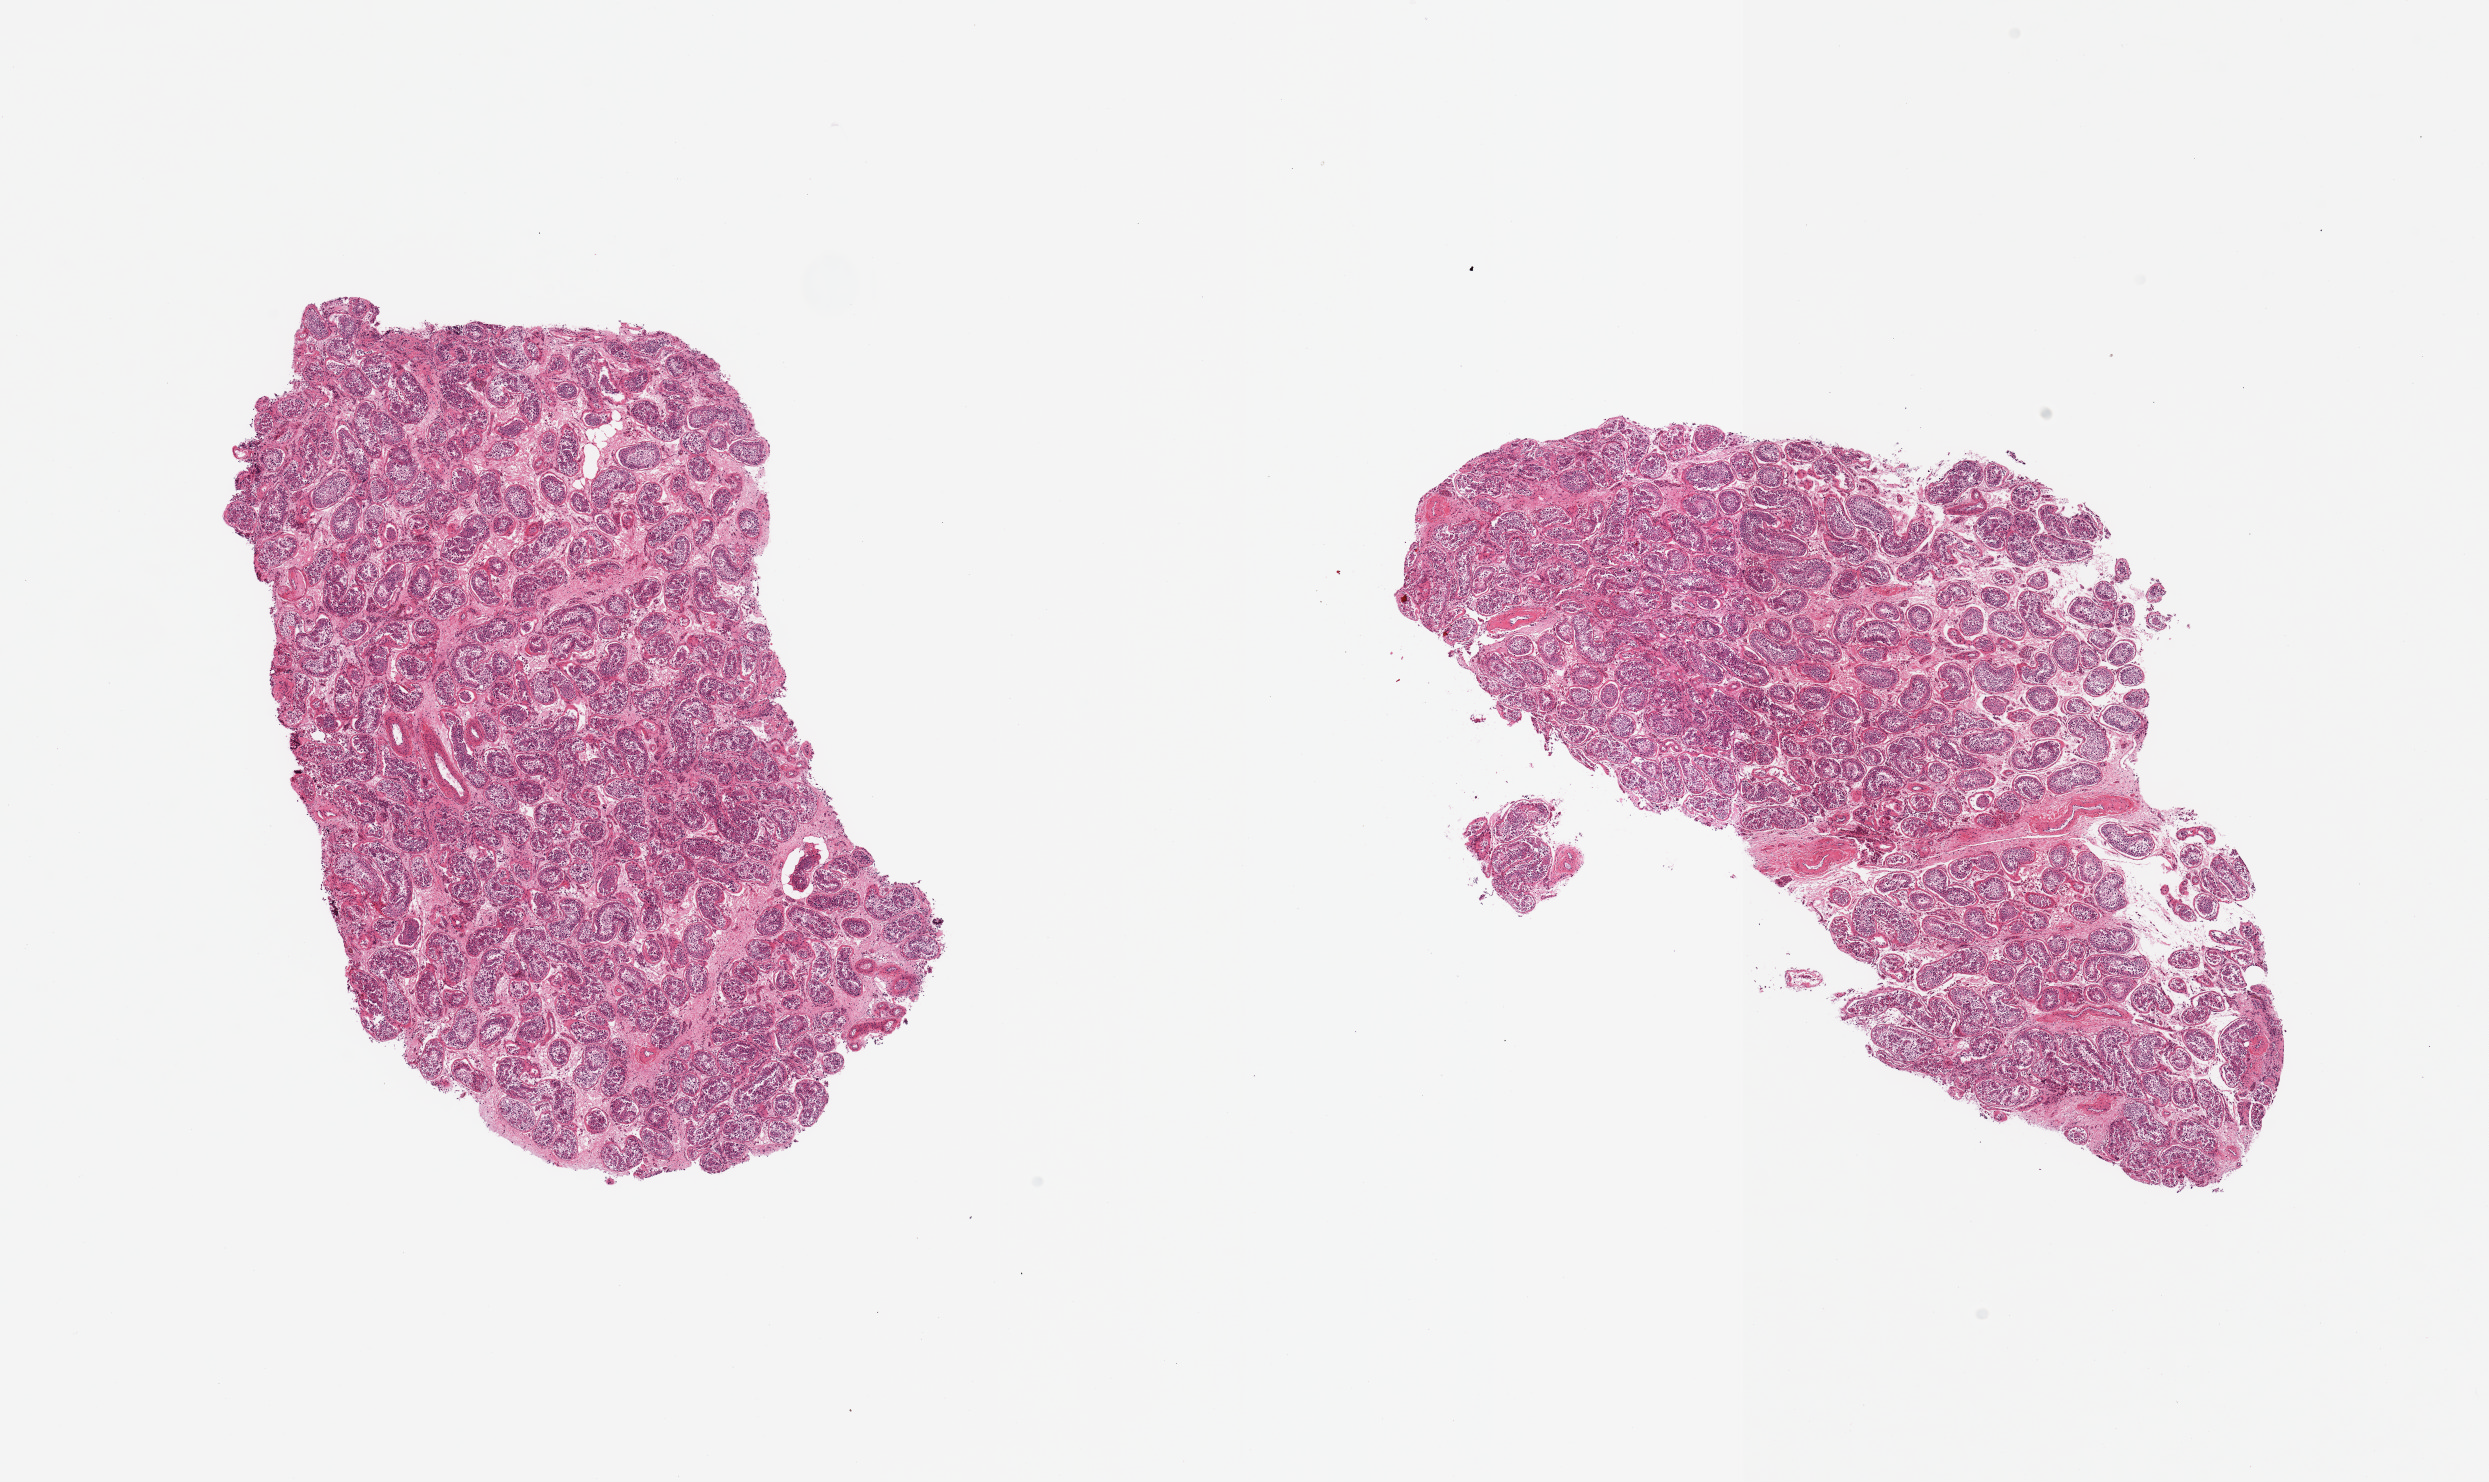
Whole-slide image, haematoxylin and eosin stain, brightfield — whole scanned area (about 19.7 x 11.7 mm, acquisition: 20x scan) shown as a low-resolution overview. PAXgene-fixed paraffin-embedded (PFPE) section. Sampled site (target tissue): testis. Donor tissue sample. Male donor.
Pathologist's review note for this sample: 2 pieces, spermatogenesis present, appears reduced.